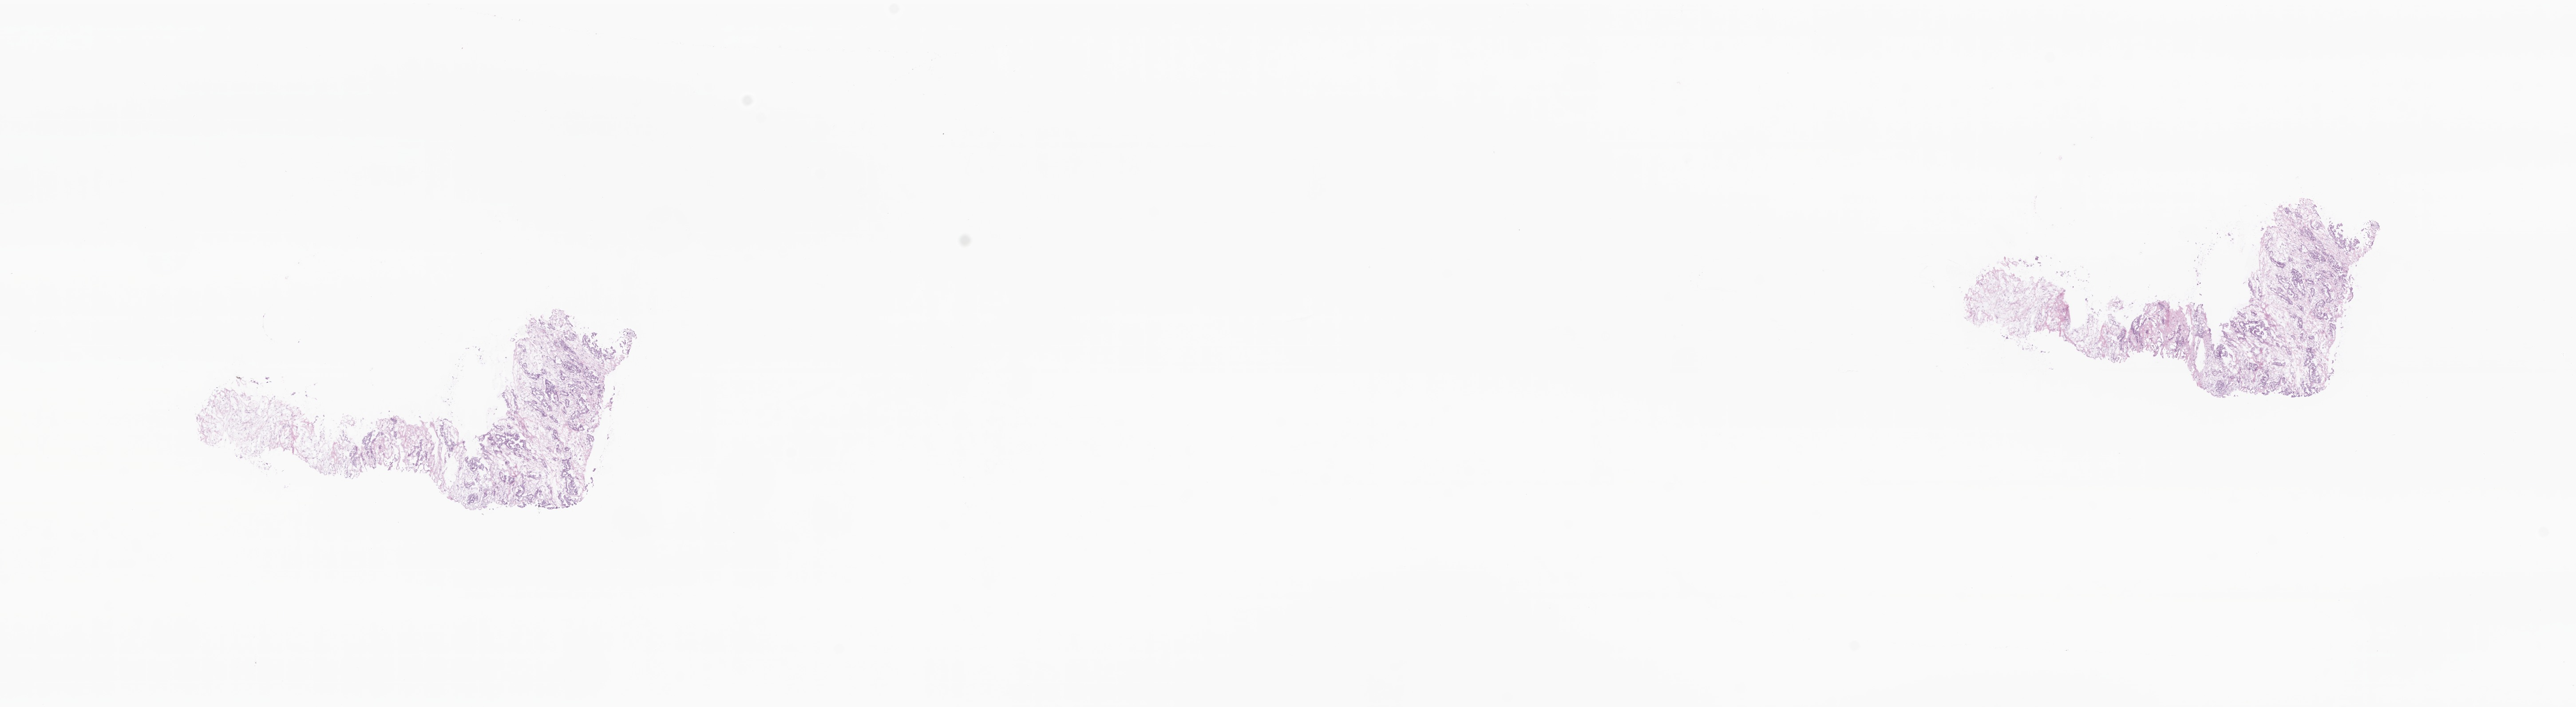
Digitized haematoxylin and eosin-stained section, whole scanned area (about 24.5 x 6.7 mm) shown as a low-resolution overview; cryosection; specimen: metastatic tumor tissue. Female patient; age at initial diagnosis 60 years. Pathologist review of this section (percent, as recorded): tumor cells 80%, tumor nuclei 80%, stromal cells 20%, necrosis 0%, normal cells 0%. Inflammatory infiltration, as recorded: lymphocyte infiltration 4%, monocyte infiltration 1%, neutrophil infiltration 5%.
Patient diagnosis (primary): Infiltrating duct carcinoma, NOS. Section: top of the tissue portion.